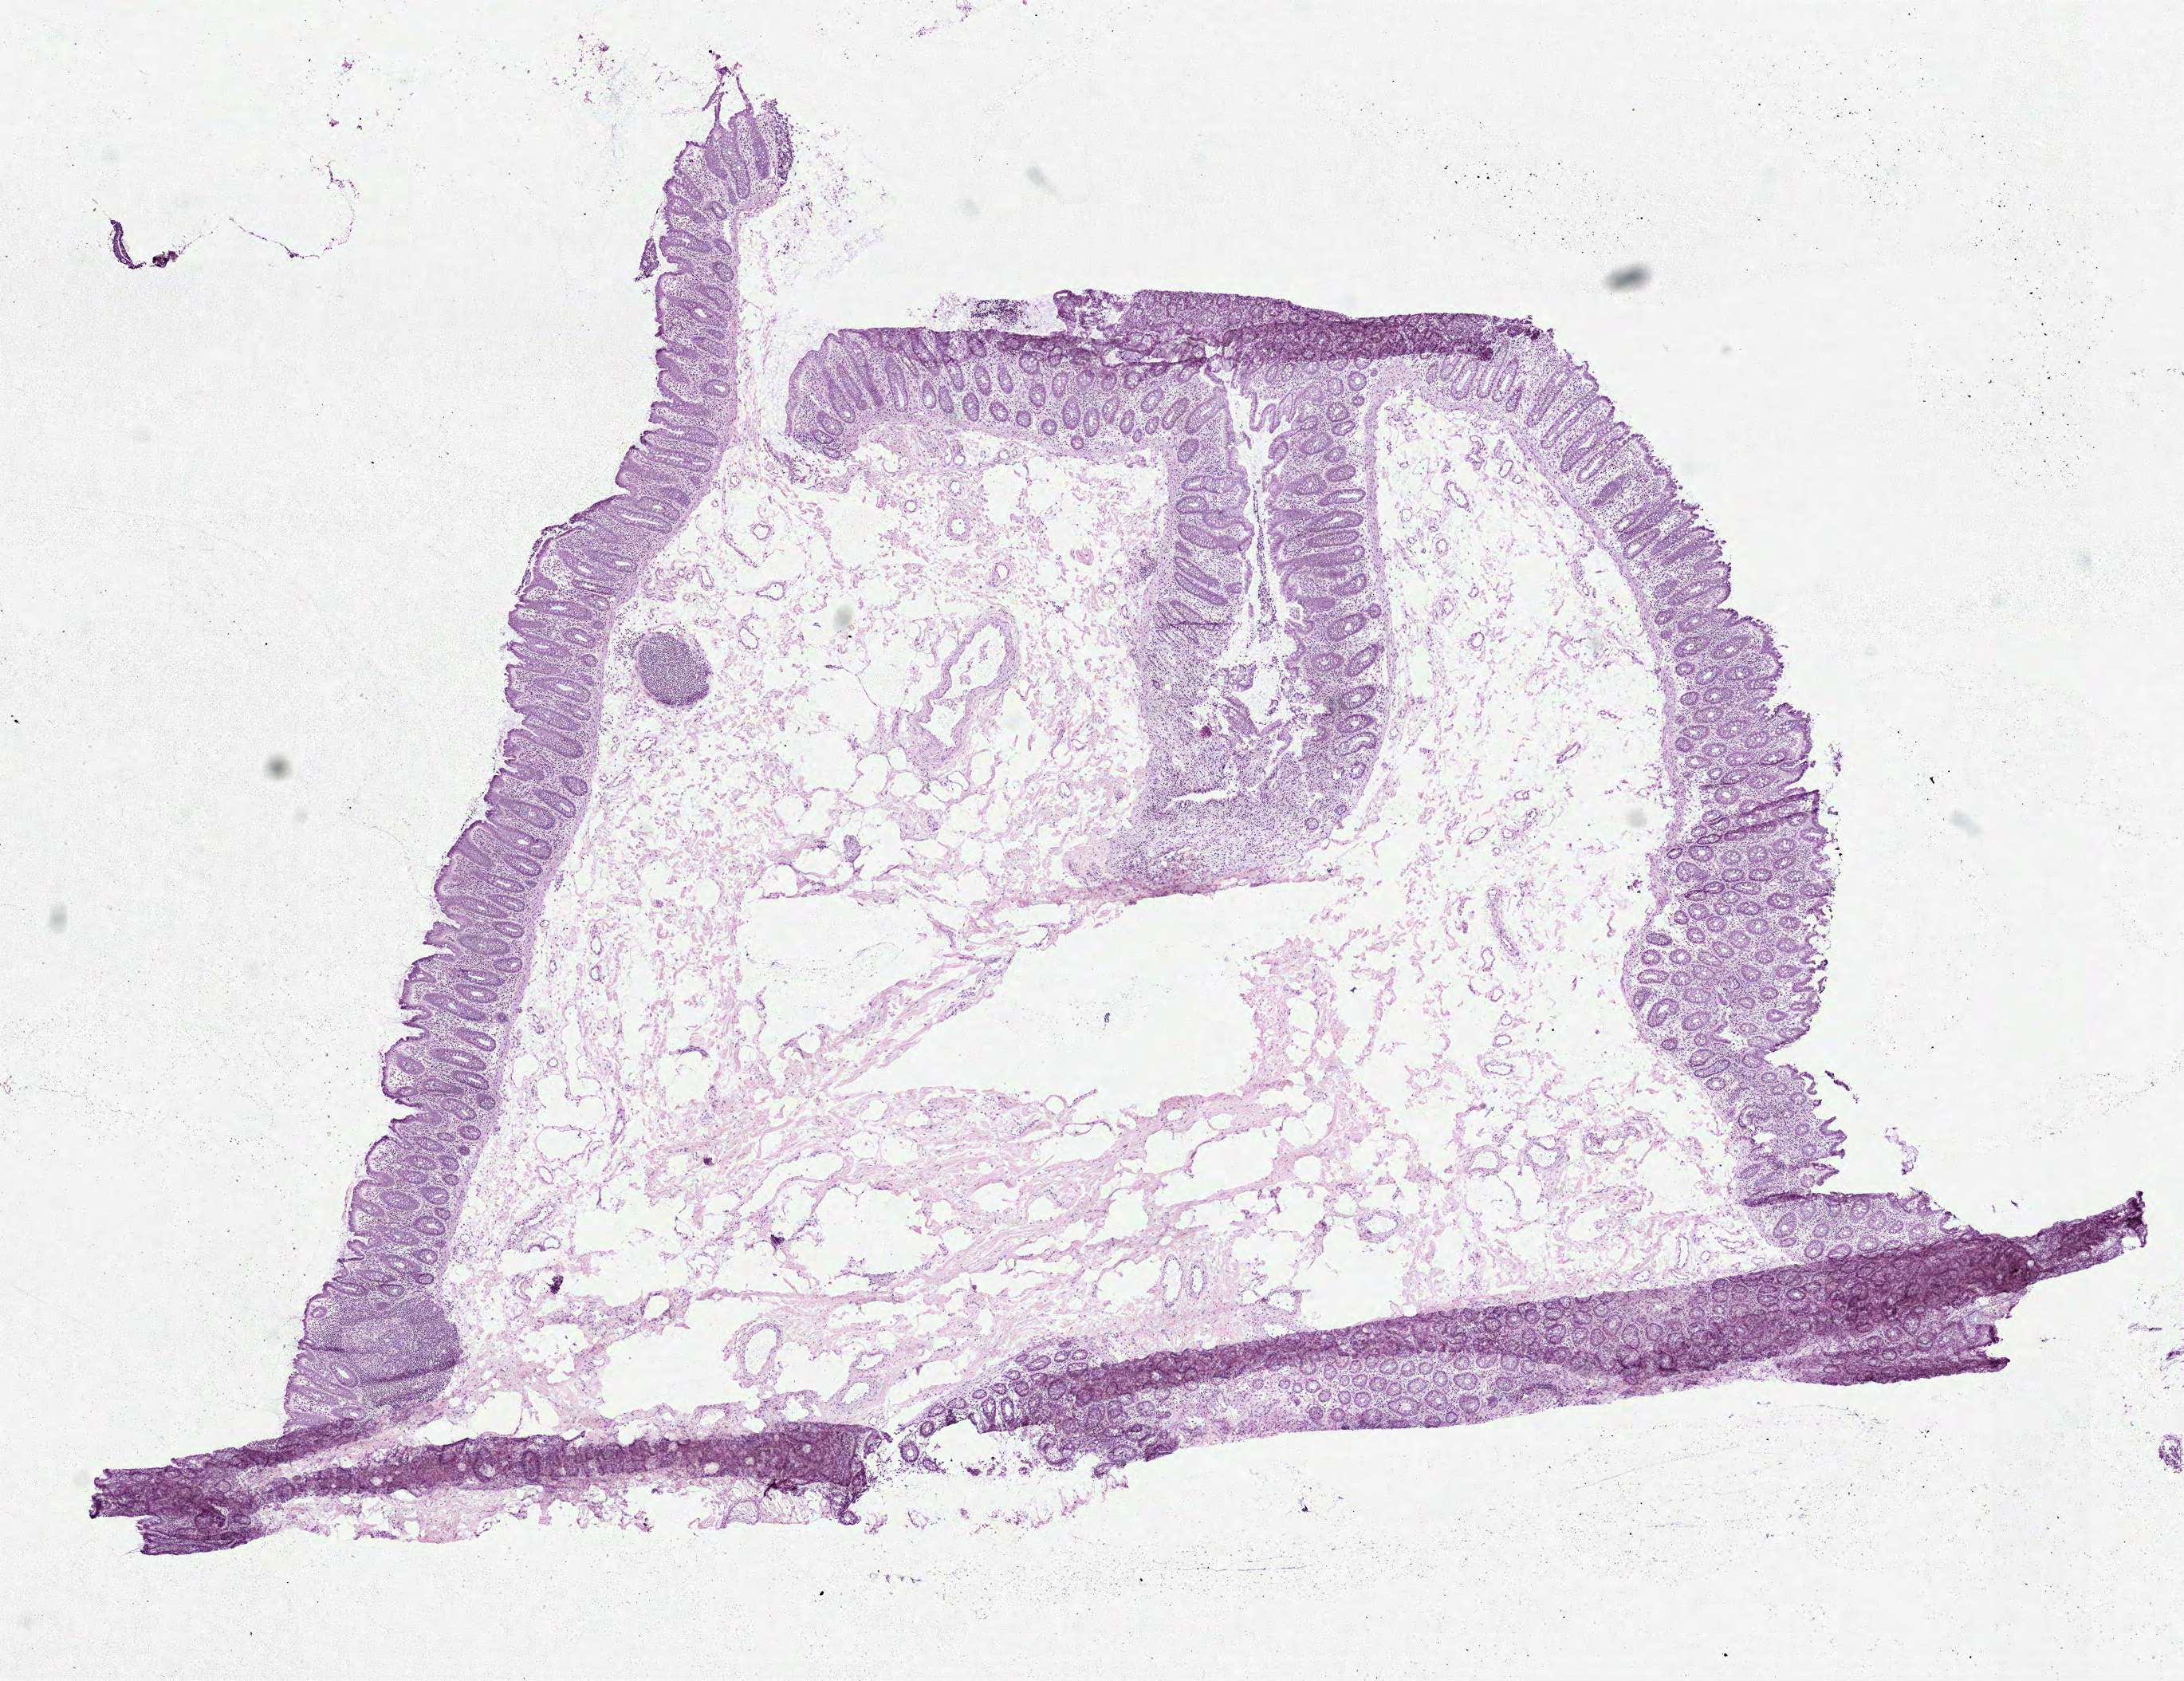
Digitized Hematoxylin and eosin (H&E) stained tissue section (whole slide), whole scanned area (about 11.0 x 8.5 mm, slide scanned at 40x) shown as a low-resolution overview. Frozen section. Colon, solid tissue normal (non-tumour tissue) sample. Male patient; age at initial diagnosis 73 years.
This section: solid tissue normal (non-tumour) sample from the same patient. Patient diagnosis: Adenocarcinoma, NOS (hepatic flexure of colon).